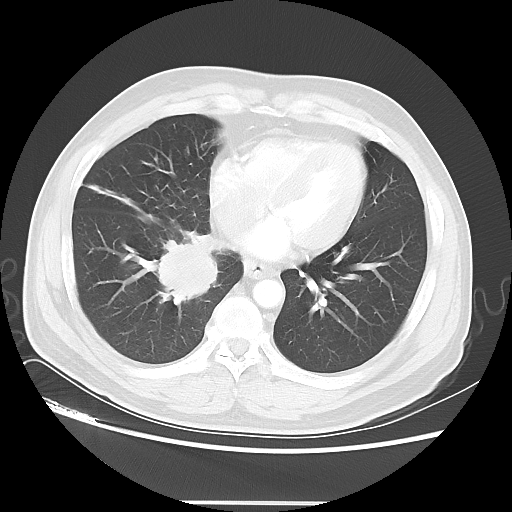
Chest CT, one axial slice; position 16 of 48 along the scan axis; reconstruction kernel LUNG; lung window (W 1500 / L -600 HU); 5 mm slice thickness; 512 × 512 image matrix, field of view 390 × 390 mm. Male patient, age 53 years. Case-level facts recorded for this patient, not image findings: clinical TNM (as recorded): T2 N3 M0; histopathological grade: G3.
Outlined on this slice (bounding box drawn by a radiologist):
- lung tumour (recorded histology: small cell carcinoma): box from (x=145, y=232) to (x=231, y=307) px